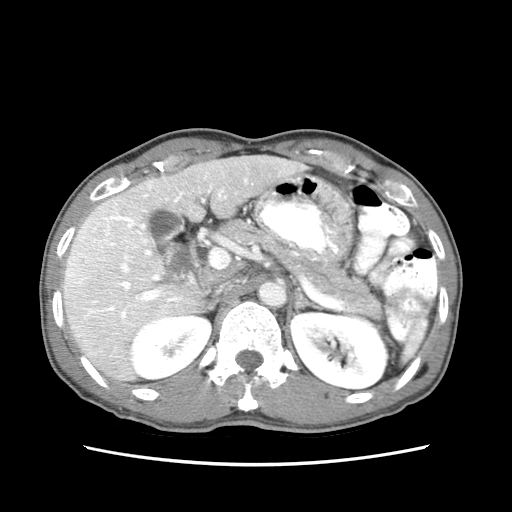
Contrast-enhanced abdominal CT (liver protocol), one axial slice; position 39 of 79 along the scan axis; soft-tissue window (W 400 / L 40 HU); 2.5 mm slice thickness; 512 × 512 image matrix, field of view 320 × 320 mm. Case-level facts recorded for this patient, not image findings: diagnosis: hepatocellular carcinoma (patient treated with transarterial chemoembolisation; whether this scan precedes or follows treatment is not stated here); TNM stage (as recorded): Stage-IIIB; Child-Pugh class: A; tumour differentiation: moderately differentiated; tumour nodularity: multinodular.
Outlined on this slice (semi-automatic segmentation, software-assisted and operator-edited):
- liver parenchyma outside the tumour (the mass and vessels are separate outlines, so this box may not span the whole liver): box from (x=62, y=153) to (x=306, y=386) px
- mass: (x=66, y=252)–(x=103, y=282)
- liver vessels: (x=65, y=168)–(x=252, y=350)